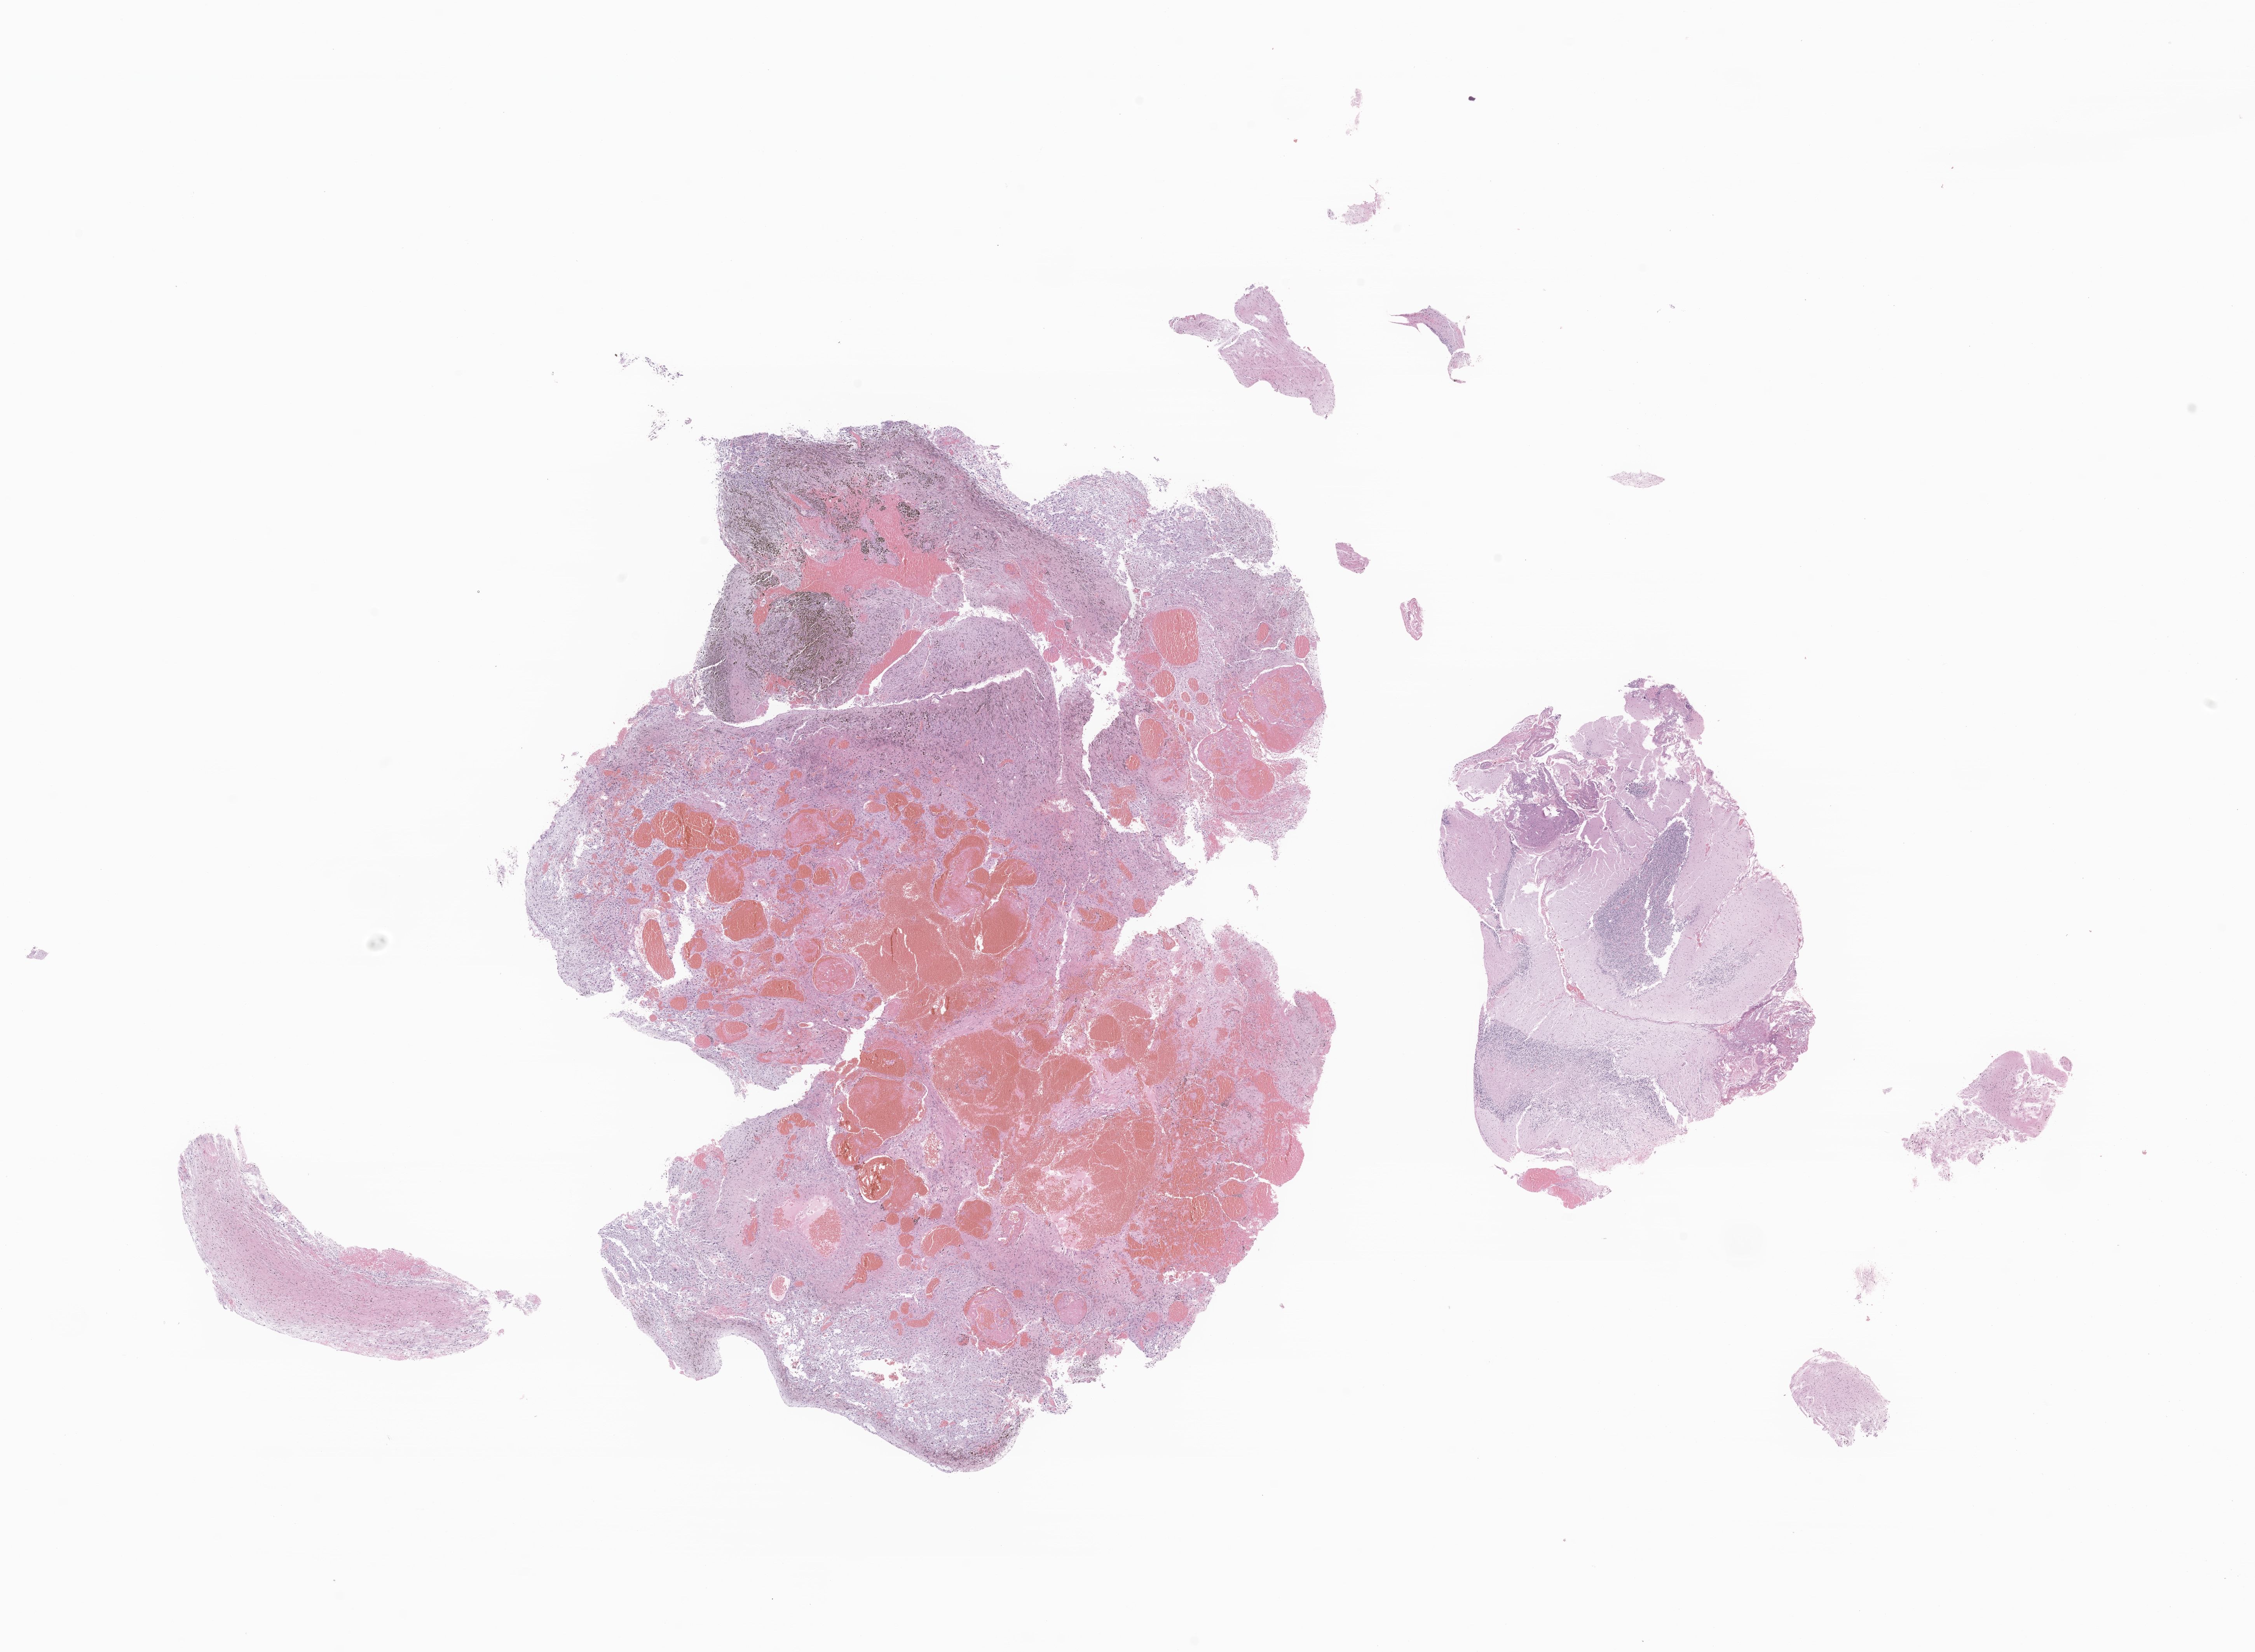
Hematoxylin and eosin (H&E) whole-slide image of tumor tissue from the cerebellum — whole scanned area (about 24.5 x 17.9 mm) shown as a low-resolution overview. Formalin-fixed, paraffin-embedded (FFPE) tissue. Patient male; age 200 months (16 years 8 months).
- diagnosis (ICD-O-3 morphology term): Pilocytic astrocytoma